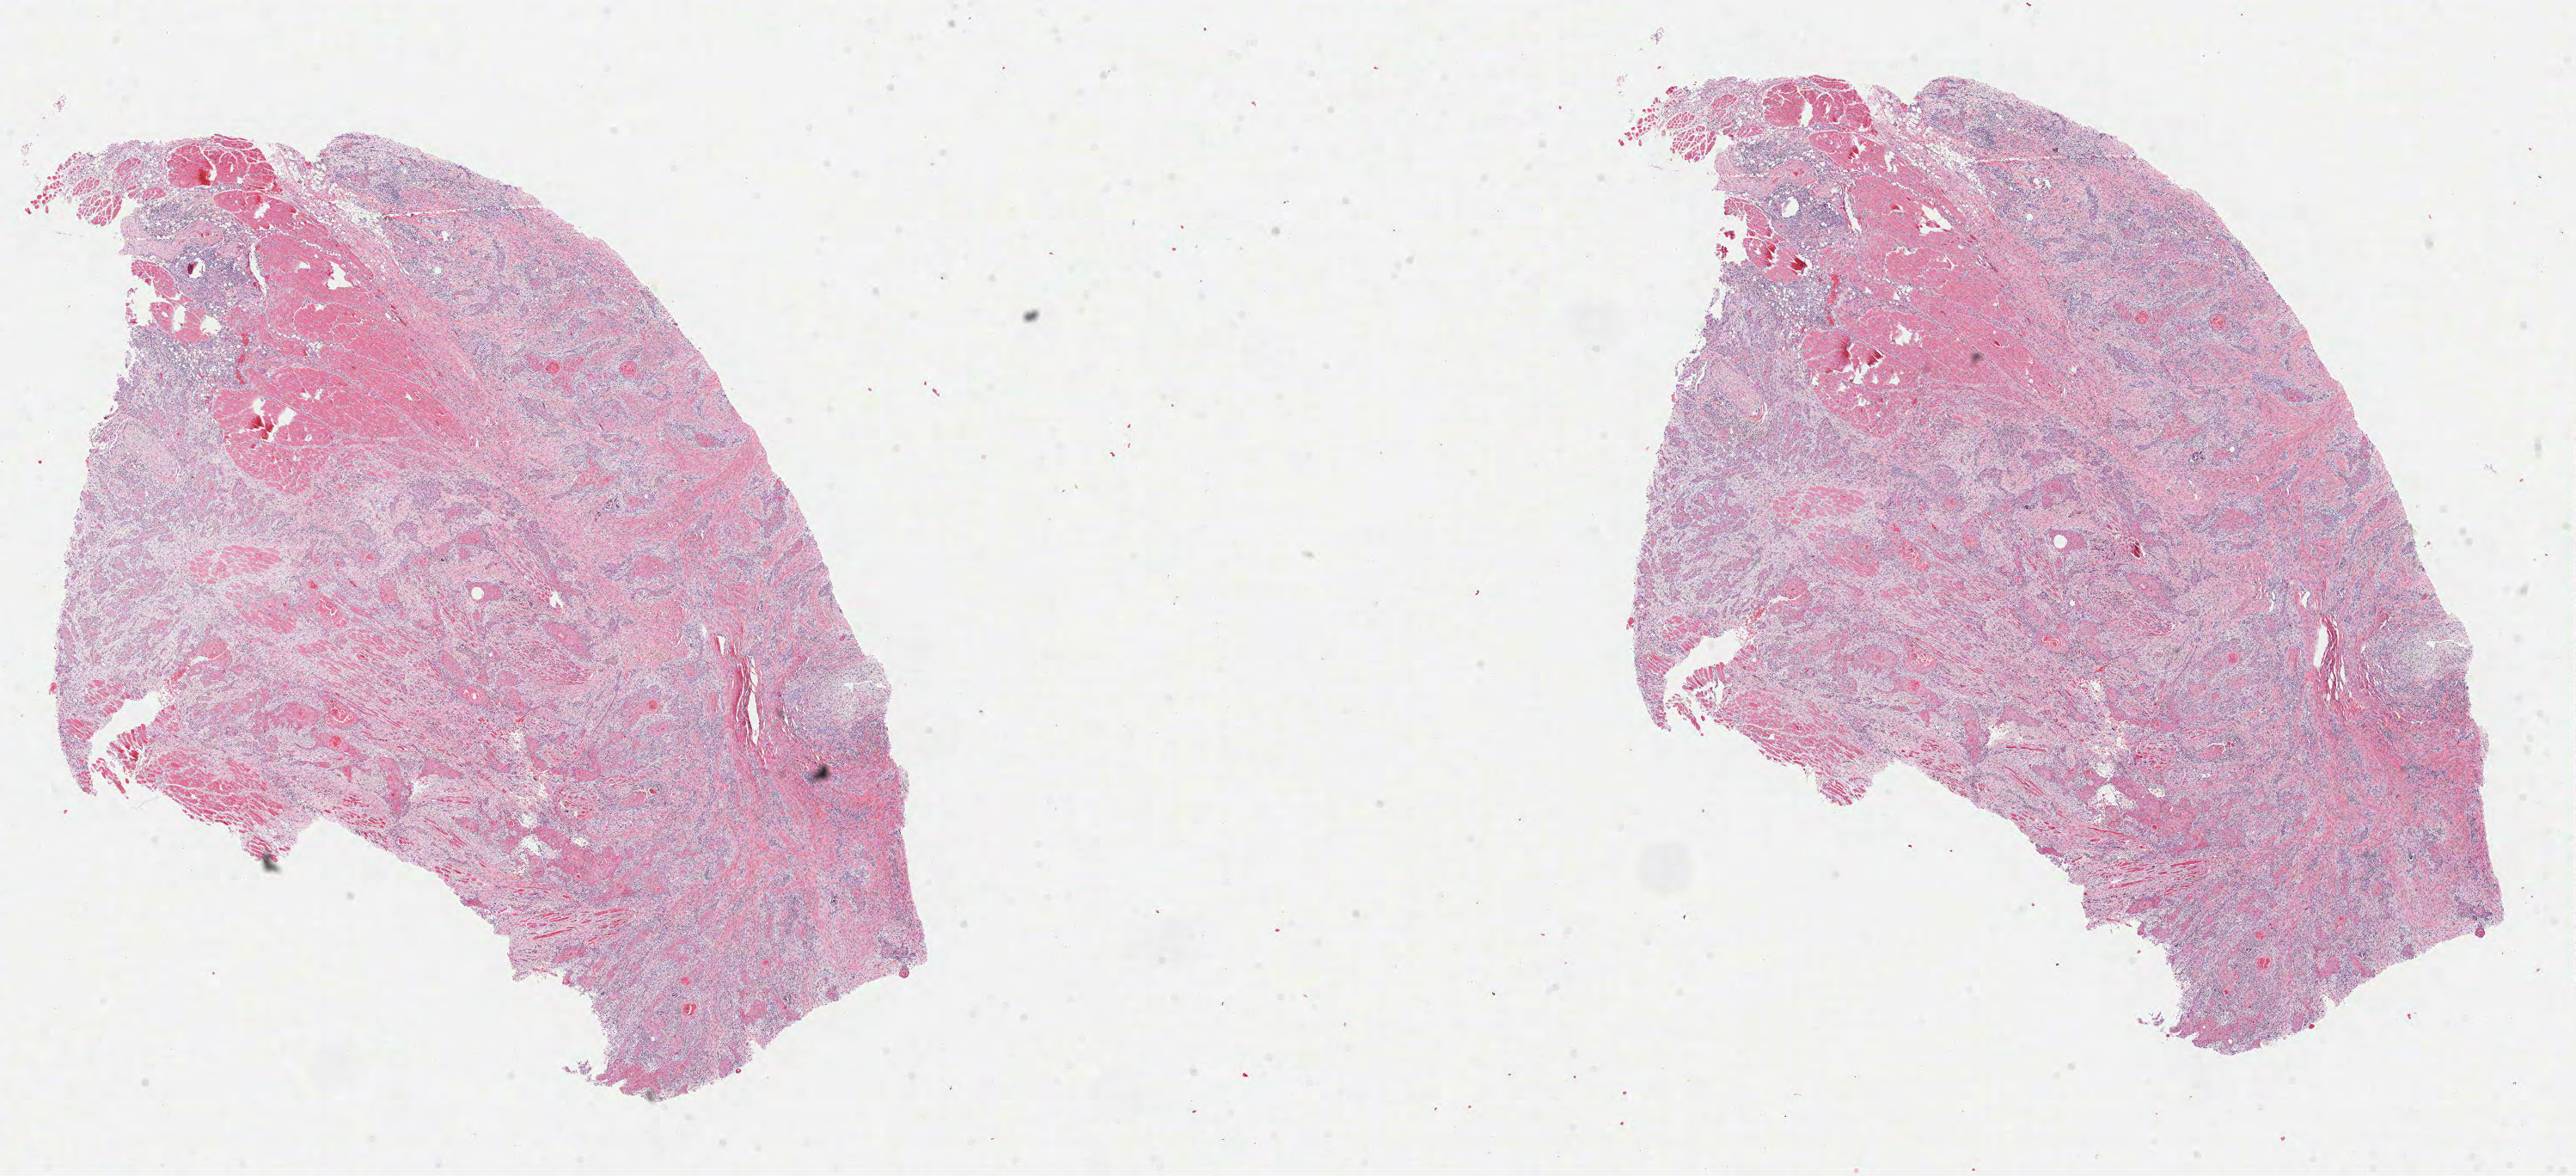
H&E-stained whole-slide image — a low-resolution overview of the entire scanned area, about 24.2 x 11.0 mm (slide scanned at 40x). Formalin-fixed paraffin-embedded (FFPE) diagnostic section. Head and neck, primary tumour sample. Male patient; age at initial diagnosis 64 years. Histologic grade: G2 (moderately differentiated).
AJCC pathologic stage: IVA (7th edition). Lymph nodes positive (case pathology): 1 of 75 examined. Histologic diagnosis: Squamous cell carcinoma, NOS (tongue, NOS).